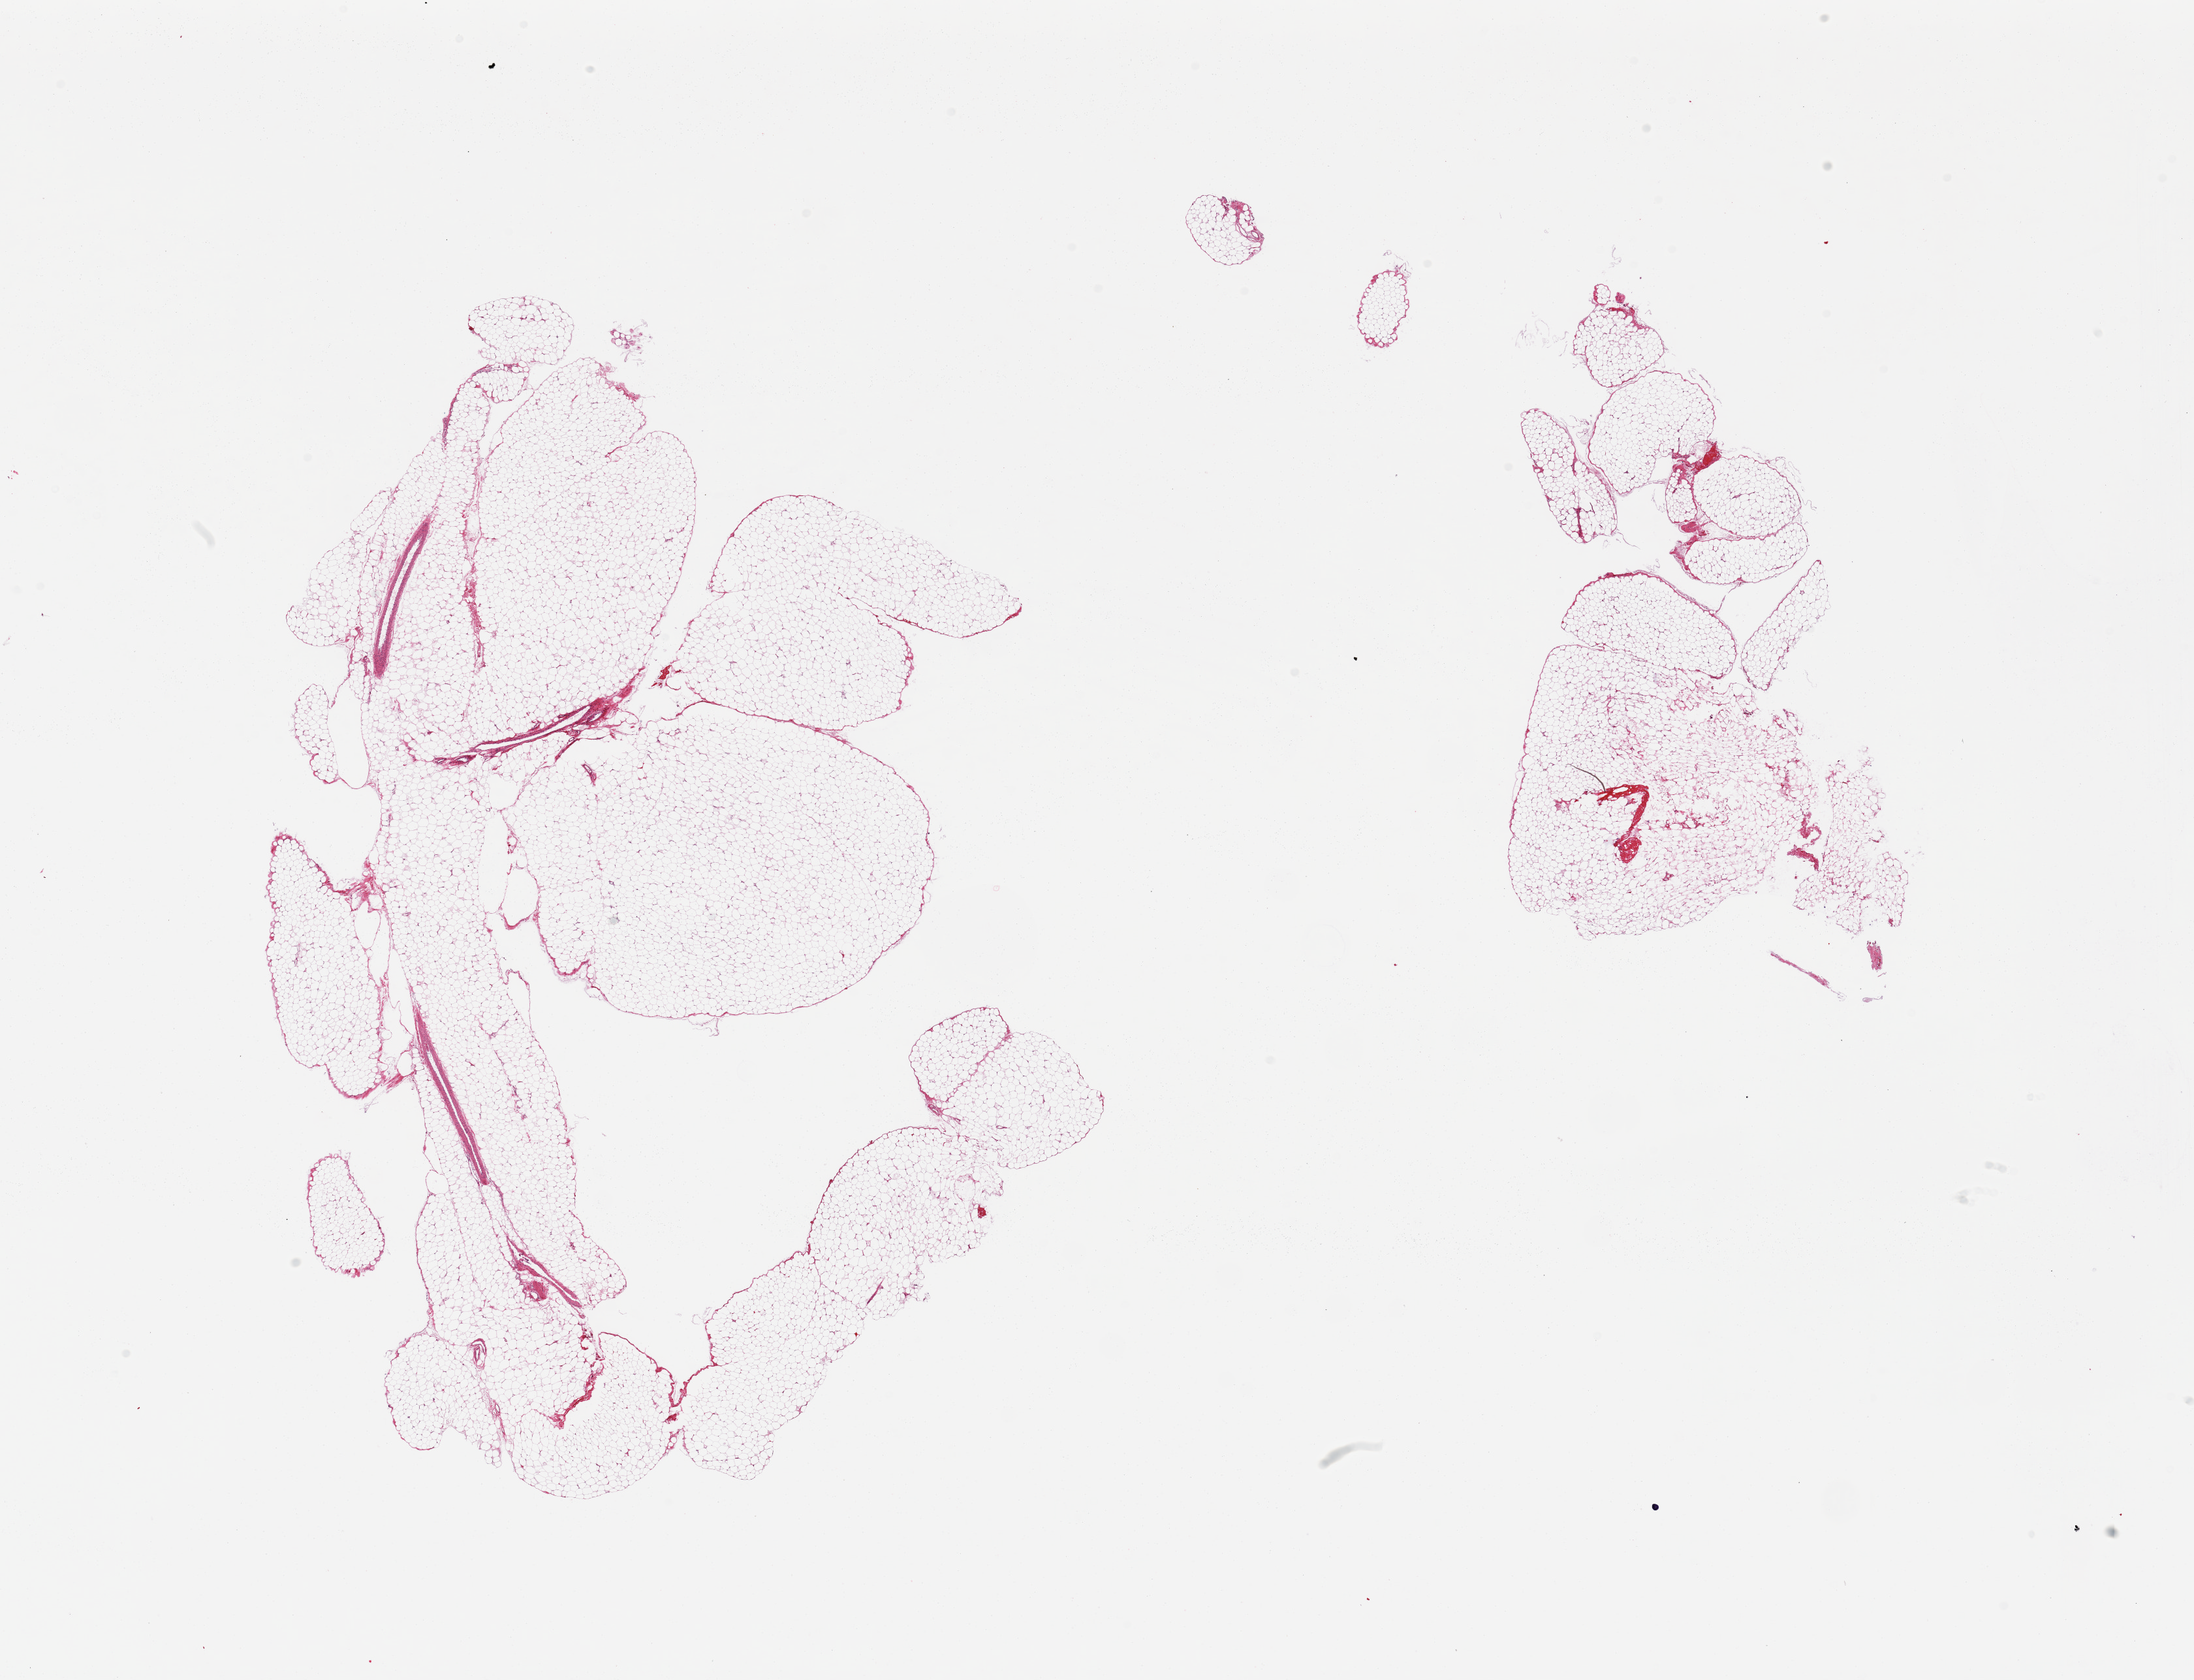
Haematoxylin and eosin whole-slide image — a low-resolution overview of the entire scanned area, about 26.6 x 20.4 mm (from a 20x scan), PAXgene-fixed paraffin-embedded (PFPE) section, section of omentum (target tissue), donor tissue sample. Donor sex: male.
Reviewer comment on this tissue sample: 2 pieces, trace interstitial vascular elements/fascia.